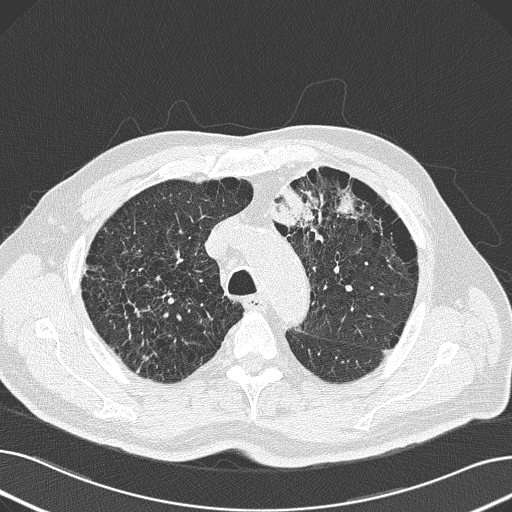
Chest CT (low-dose screening protocol), one axial image, baseline annual screen, lung window (W 1500 / L -600 HU), lung (sharp) reconstruction kernel (B50f), slice 51 of 165 in the series, 512 × 512 image matrix, field of view 370 × 370 mm. Male participant, aged 69 years at enrolment. Former smoker at enrolment.
Expert-annotated lung lesion, bounding box <224,151,378,255> (left, top, right, bottom; pixels). Screening reader's record for this exam (one nodule recorded; not confirmed to be the boxed lesion): non-calcified nodule or mass ≥4 mm, left upper lobe, 6 × 10 mm, spiculated (stellate) margins, soft tissue attenuation. Lung cancer was diagnosed 20 days after this screen: non-small cell carcinoma, left upper lobe, poorly differentiated (G3), stage IB (AJCC 6th edition), 100 mm at pathology.